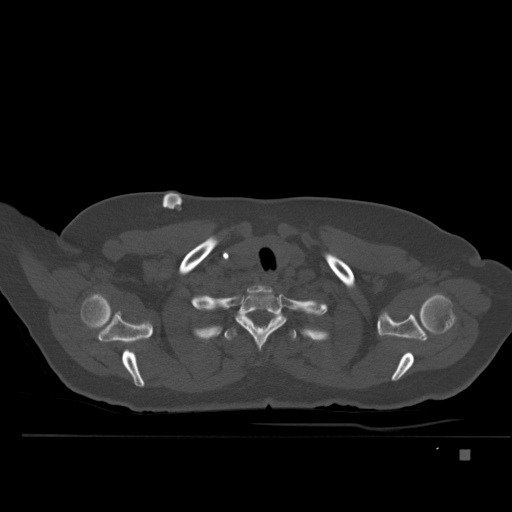
CT including the spine, one axial slice; slice 400 of 477 in the series (ordered by position); bone window (W 1800 / L 400 HU); 1.5 mm slice thickness; 512 × 512 image matrix, field of view 422 × 422 mm. Patient: female, 74 years. From the clinical record (not read from this slice): primary cancer: colon.
Structures marked on this image (semi-automatically segmented with operator editing):
- T1 vertebra: bounding box [x1, y1, x2, y2] px = [237, 291, 285, 347]
- T2 vertebra: [198, 321, 315, 342]